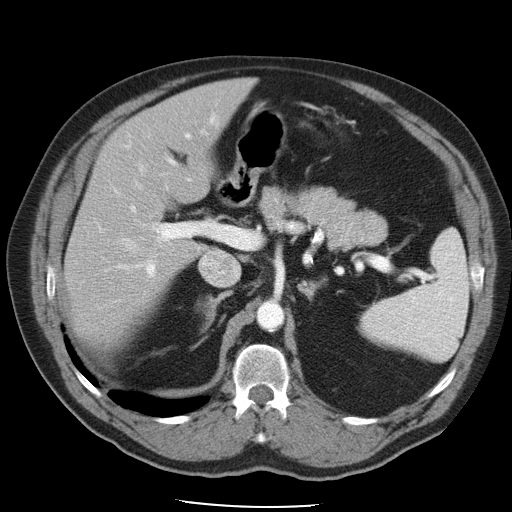
Contrast-enhanced abdominal CT, one axial slice; slice 30 of 49 in the series (ordered by position); reconstruction kernel STANDARD; 120 kVp; soft-tissue window (W 400 / L 40 HU); 5 mm slice thickness; 512 × 512 image matrix, field of view 395 × 395 mm. Male patient, age 68 years. From the clinical record (not read from this slice): diagnosis: colorectal cancer liver metastases, imaged before liver resection; multiple liver metastases: yes; largest metastasis: 1.7 cm.
Outlined on this slice (outlined manually by an expert reader):
- hepatic veins: box from (x=116, y=162) to (x=239, y=285) px
- liver: (x=66, y=79)–(x=253, y=350)
- planned liver remnant (the part of the liver to remain after resection): (x=67, y=79)–(x=253, y=351)
- portal vein (with intrahepatic branches): (x=98, y=116)–(x=217, y=278)